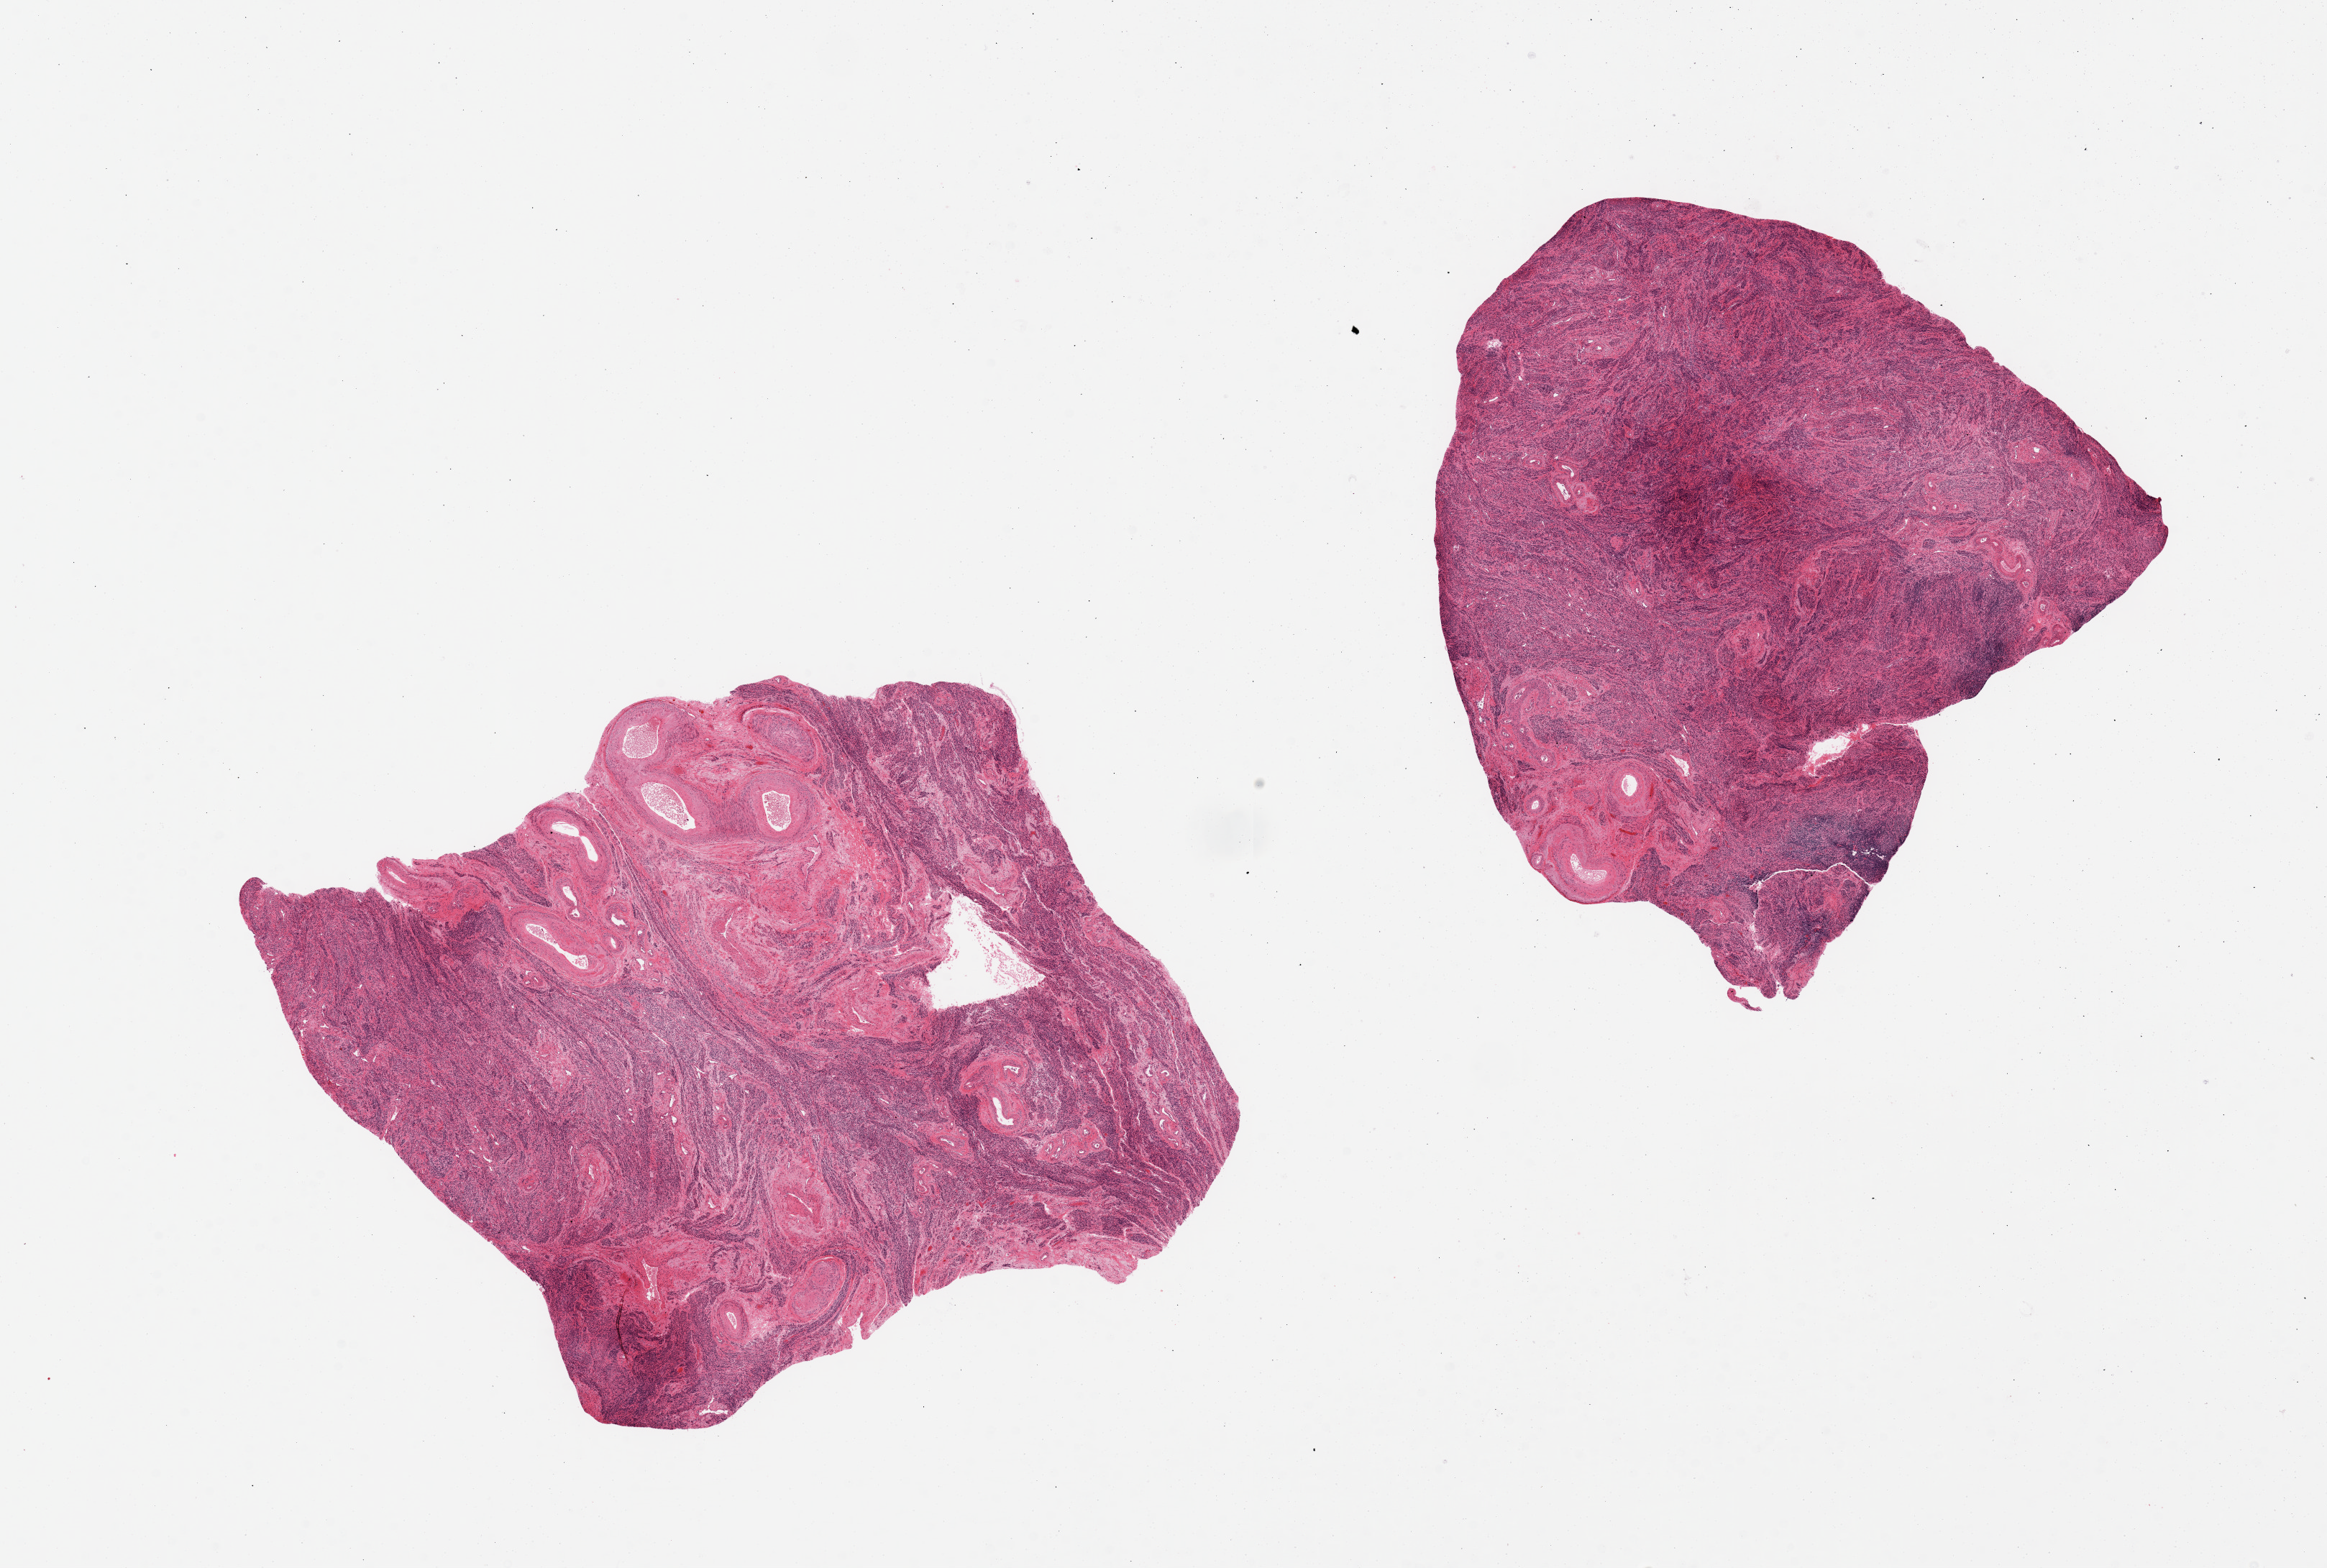
Digitized haematoxylin and eosin-stained section, brightfield — a low-resolution overview of the entire scanned area, about 25.6 x 17.3 mm (slide scanned at 20x); PAXgene-fixed, paraffin-embedded tissue; section of uterus (target tissue); donor tissue sample. Female donor.
Reviewer comment on this tissue sample: 2 pieces, myometrial tissue; no ovarian parenchyma present.